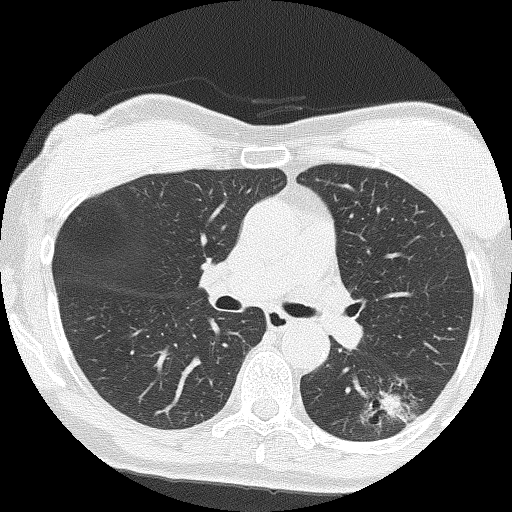
Axial slice from a low-dose chest CT screening exam, second annual screen, lung window (W 1500 / L -600 HU), lung (sharp) reconstruction kernel (FC51), slice 64 of 159 in the series, 512 × 512 image matrix, field of view 303 × 303 mm. Female participant, aged 64 years at enrolment. Former smoker at enrolment.
Lesion marked by an expert reader, bounding box (x1, y1, x2, y2) in pixels: (357, 375, 433, 439). The screening reader recorded 3 non-calcified nodules or masses ≥4 mm on this exam (right upper lobe, right upper lobe, right middle lobe); which of them this box marks is not recorded. Participant outcome: lung cancer diagnosed 576 days after this screen — adenocarcinoma, NOS, left lower lobe, moderately differentiated (G2), stage IA (AJCC 6th edition), 17 mm at pathology.